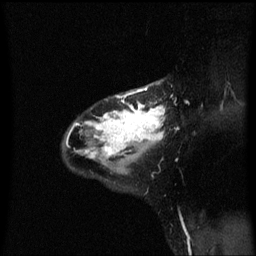
Breast MRI (dynamic contrast-enhanced), one sagittal slice; slice 43 of 60 in the series (ordered by position); dynamic contrast-enhanced series, image 2 of 3 at this slice position (ordered by acquisition); 1.5 T; TE 4.2 ms, TR 8.4 ms; 2 mm slice thickness; 256 × 256 image matrix, field of view 200 × 200 mm. Female patient, age 32 years.
Annotated regions visible in this slice (semi-automatic segmentation, software-assisted and operator-edited):
- analysis volume of interest (the breast-tissue region the enhancement analysis was run in; not a lesion): box from (x=64, y=82) to (x=167, y=167) px
- tumour enhancement mask (voxels above the 70 % enhancement threshold inside the analysis volume of interest): (x=67, y=88)–(x=166, y=159)